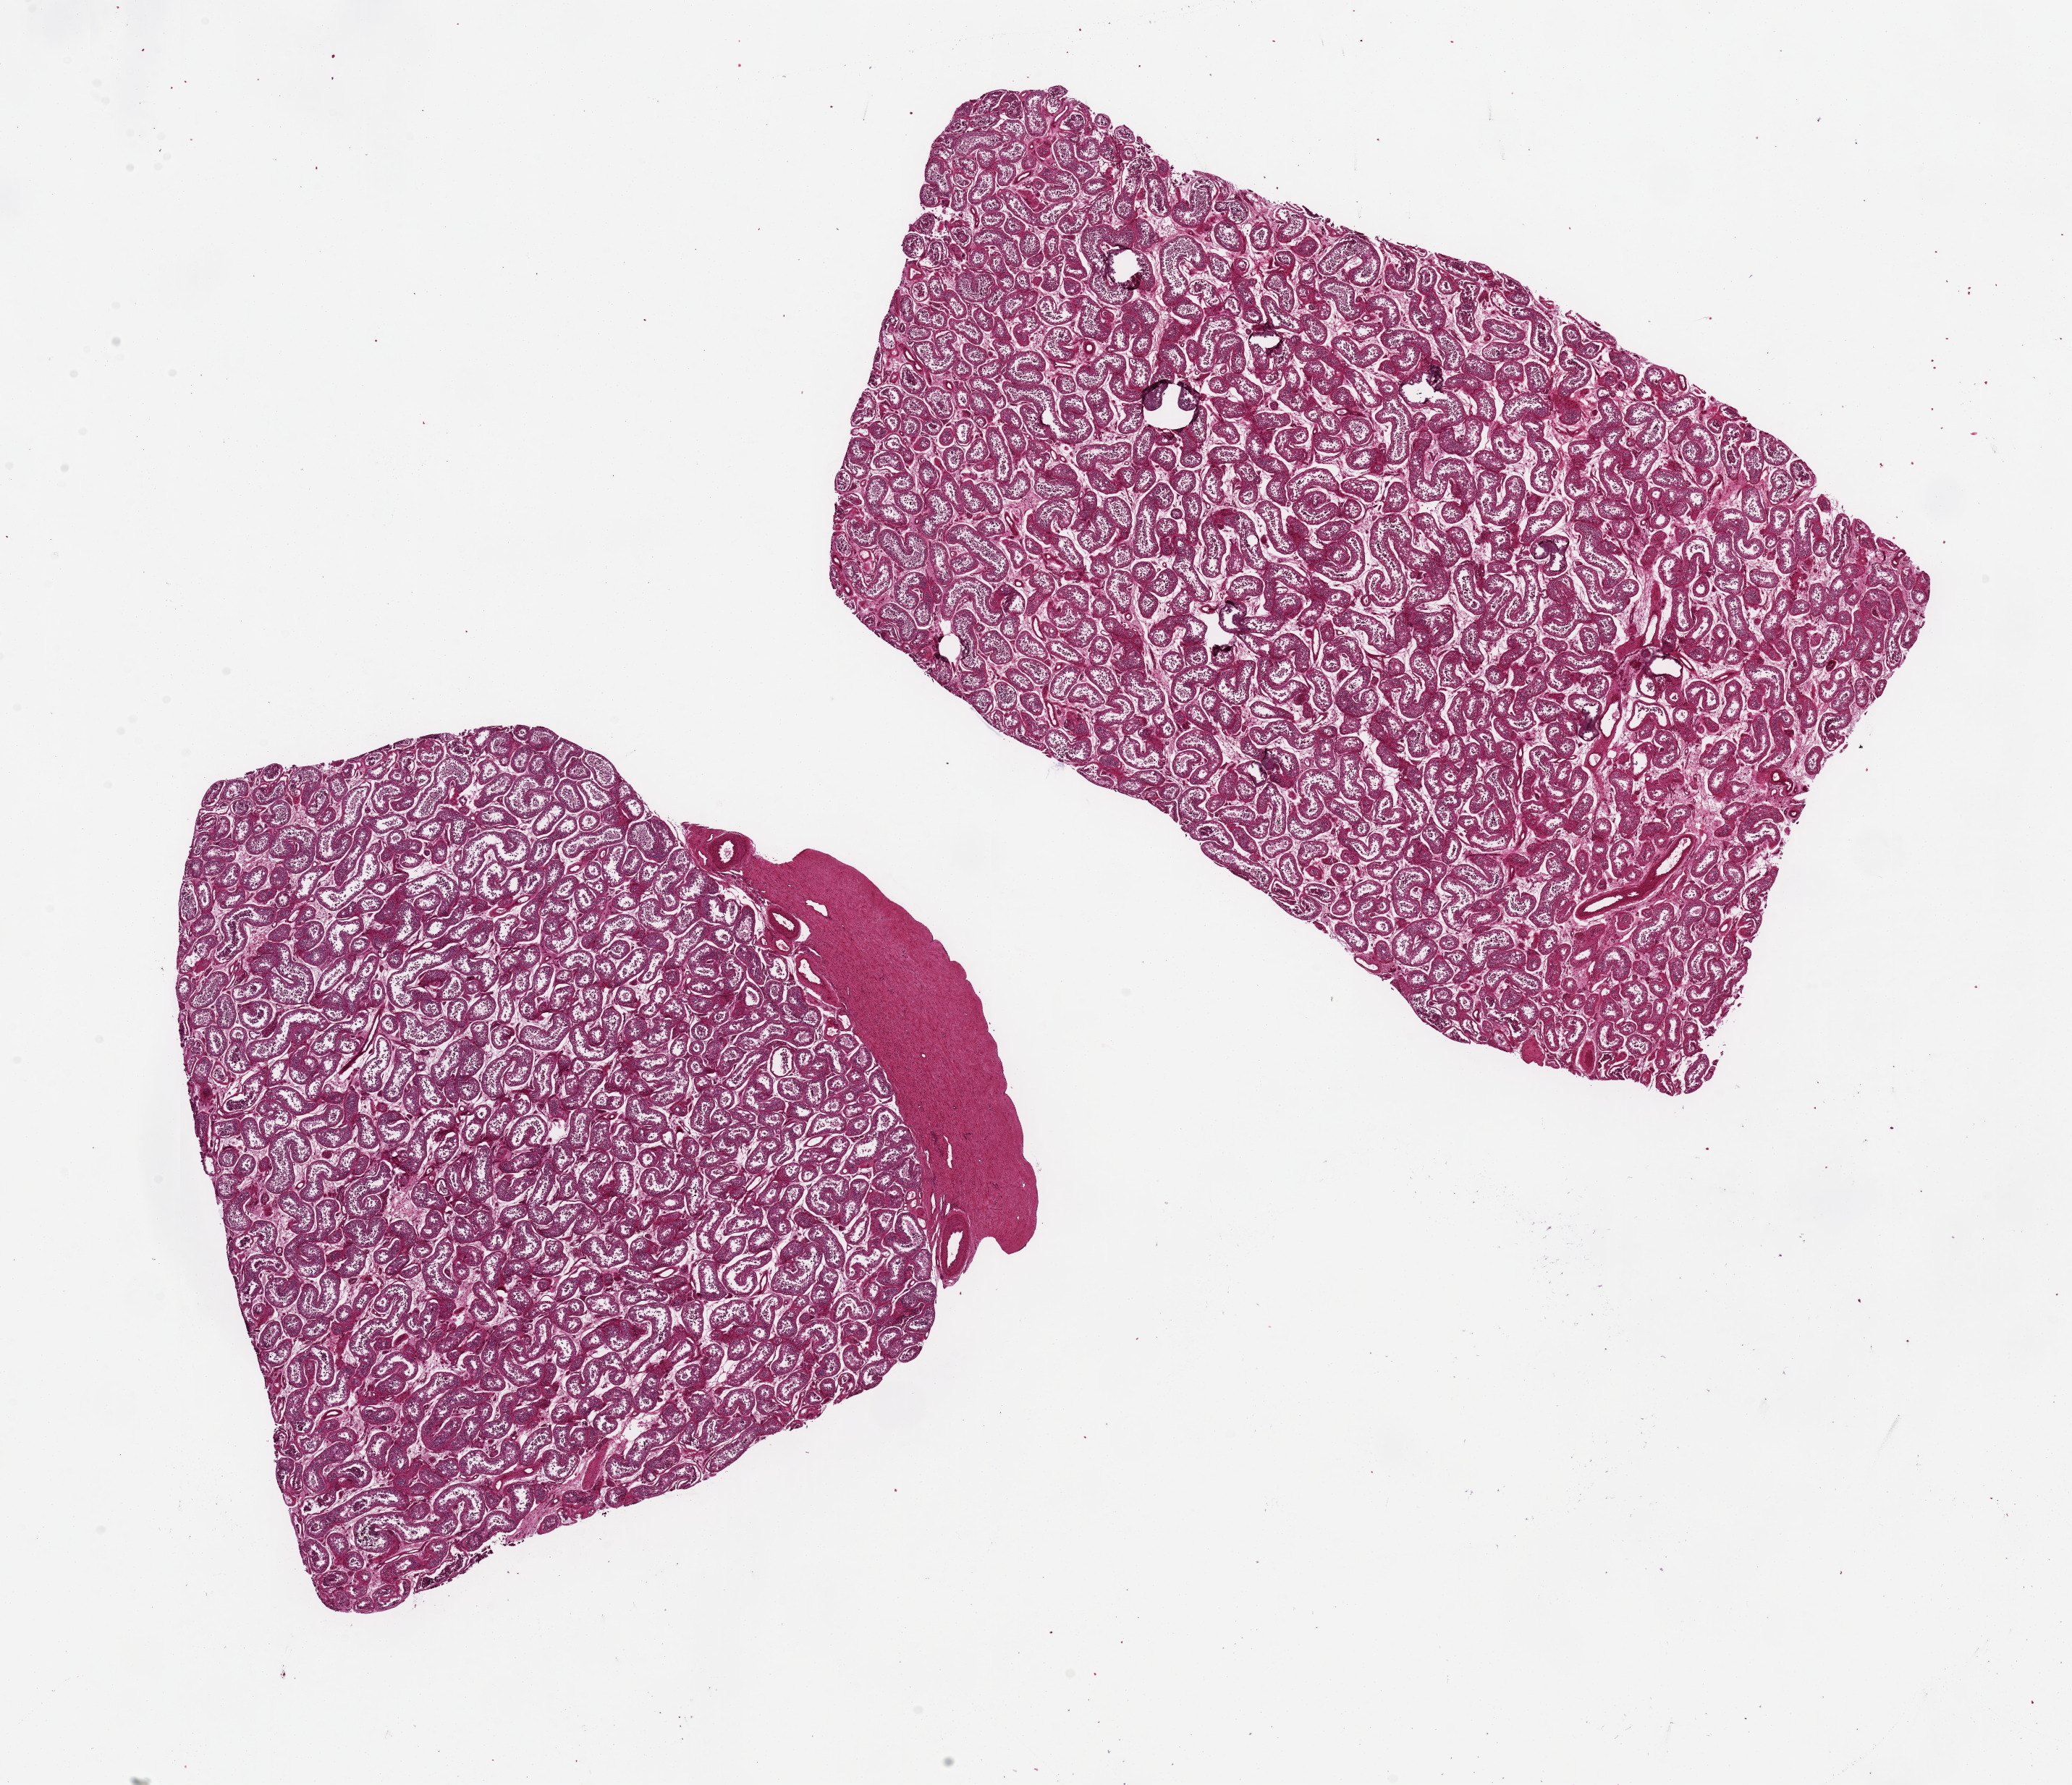
Whole-slide image, haematoxylin and eosin stain, shown as a low-resolution overview of the whole scanned area (about 22.6 x 19.5 mm, from a 20x scan). PAXgene-fixed paraffin-embedded (PFPE) section. Section of testis (target tissue). Tissue donor sample.
Pathologist's review note for this sample: 2 pieces 12x7 & 9x8 mm; 5x1 mm capsule along one edge; reduced spermatogenesis.